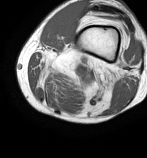
MRI of an extremity soft-tissue mass, one axial slice. Position 16 of 86 along the scan axis. MR volume resampled by the dataset authors to the PET/CT grid (not the native acquisition matrix). 3.27 mm slice thickness. 147 × 158 image matrix, field of view 144 × 154 mm. Male patient. Case-level facts recorded for this patient, not image findings: histological type: undifferentiated pleomorphic liposarcoma; grade: high; site of the primary tumour: left thigh.
Outlined on this slice (expert contour drawn on MRI and transferred to this co-registered scan by the dataset authors):
- gross tumour volume including surrounding oedema: bounding box (x1, y1, x2, y2) in pixels: (37, 58, 115, 91)